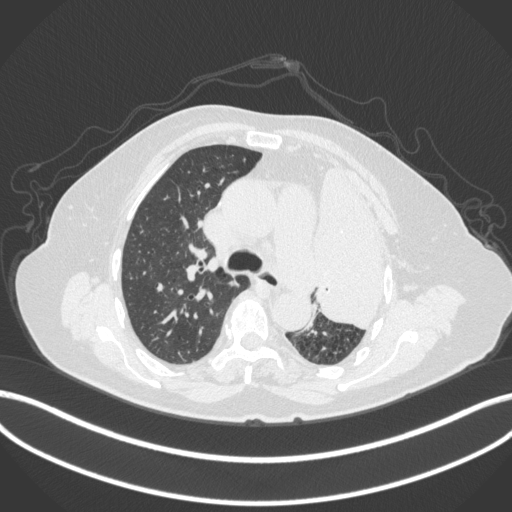
Chest CT, one axial slice. Slice 260 of 399 in the series (ordered by position). Reconstruction kernel B31f. Lung window (W 1500 / L -600 HU). 1 mm slice thickness. 512 × 512 image matrix, field of view 400 × 400 mm. Patient: female, 75 years. Case-level facts recorded for this patient, not image findings: clinical TNM (as recorded): T3 N3 M1.
Structures marked on this image (bounding box drawn by a radiologist):
- lung tumour (recorded histology: adenocarcinoma): bounding box <306,157,399,337> (left, top, right, bottom; pixels)